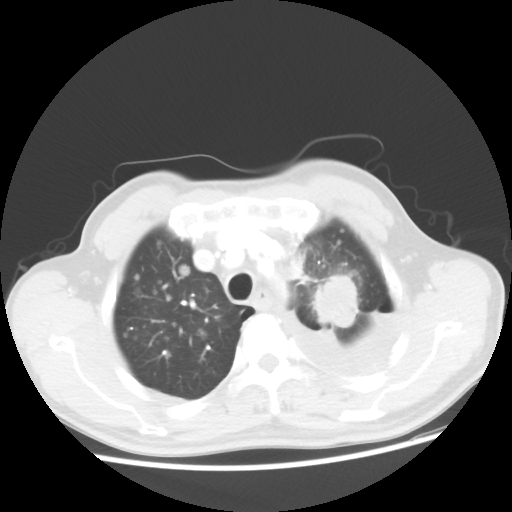
Chest CT, one axial slice. Position 39 of 48 along the scan axis. Reconstruction kernel STANDARD. Lung window (W 1500 / L -600 HU). 5 mm slice thickness. 512 × 512 image matrix. Male patient, age 55 years. From the clinical record (not read from this slice): clinical TNM (as recorded): T2 N3 M1a; histopathological grade: G3.
Annotated regions visible in this slice (rectangle marked by the reading radiologist):
- lung tumour (recorded histology: squamous cell carcinoma): box from (x=313, y=270) to (x=358, y=342) px